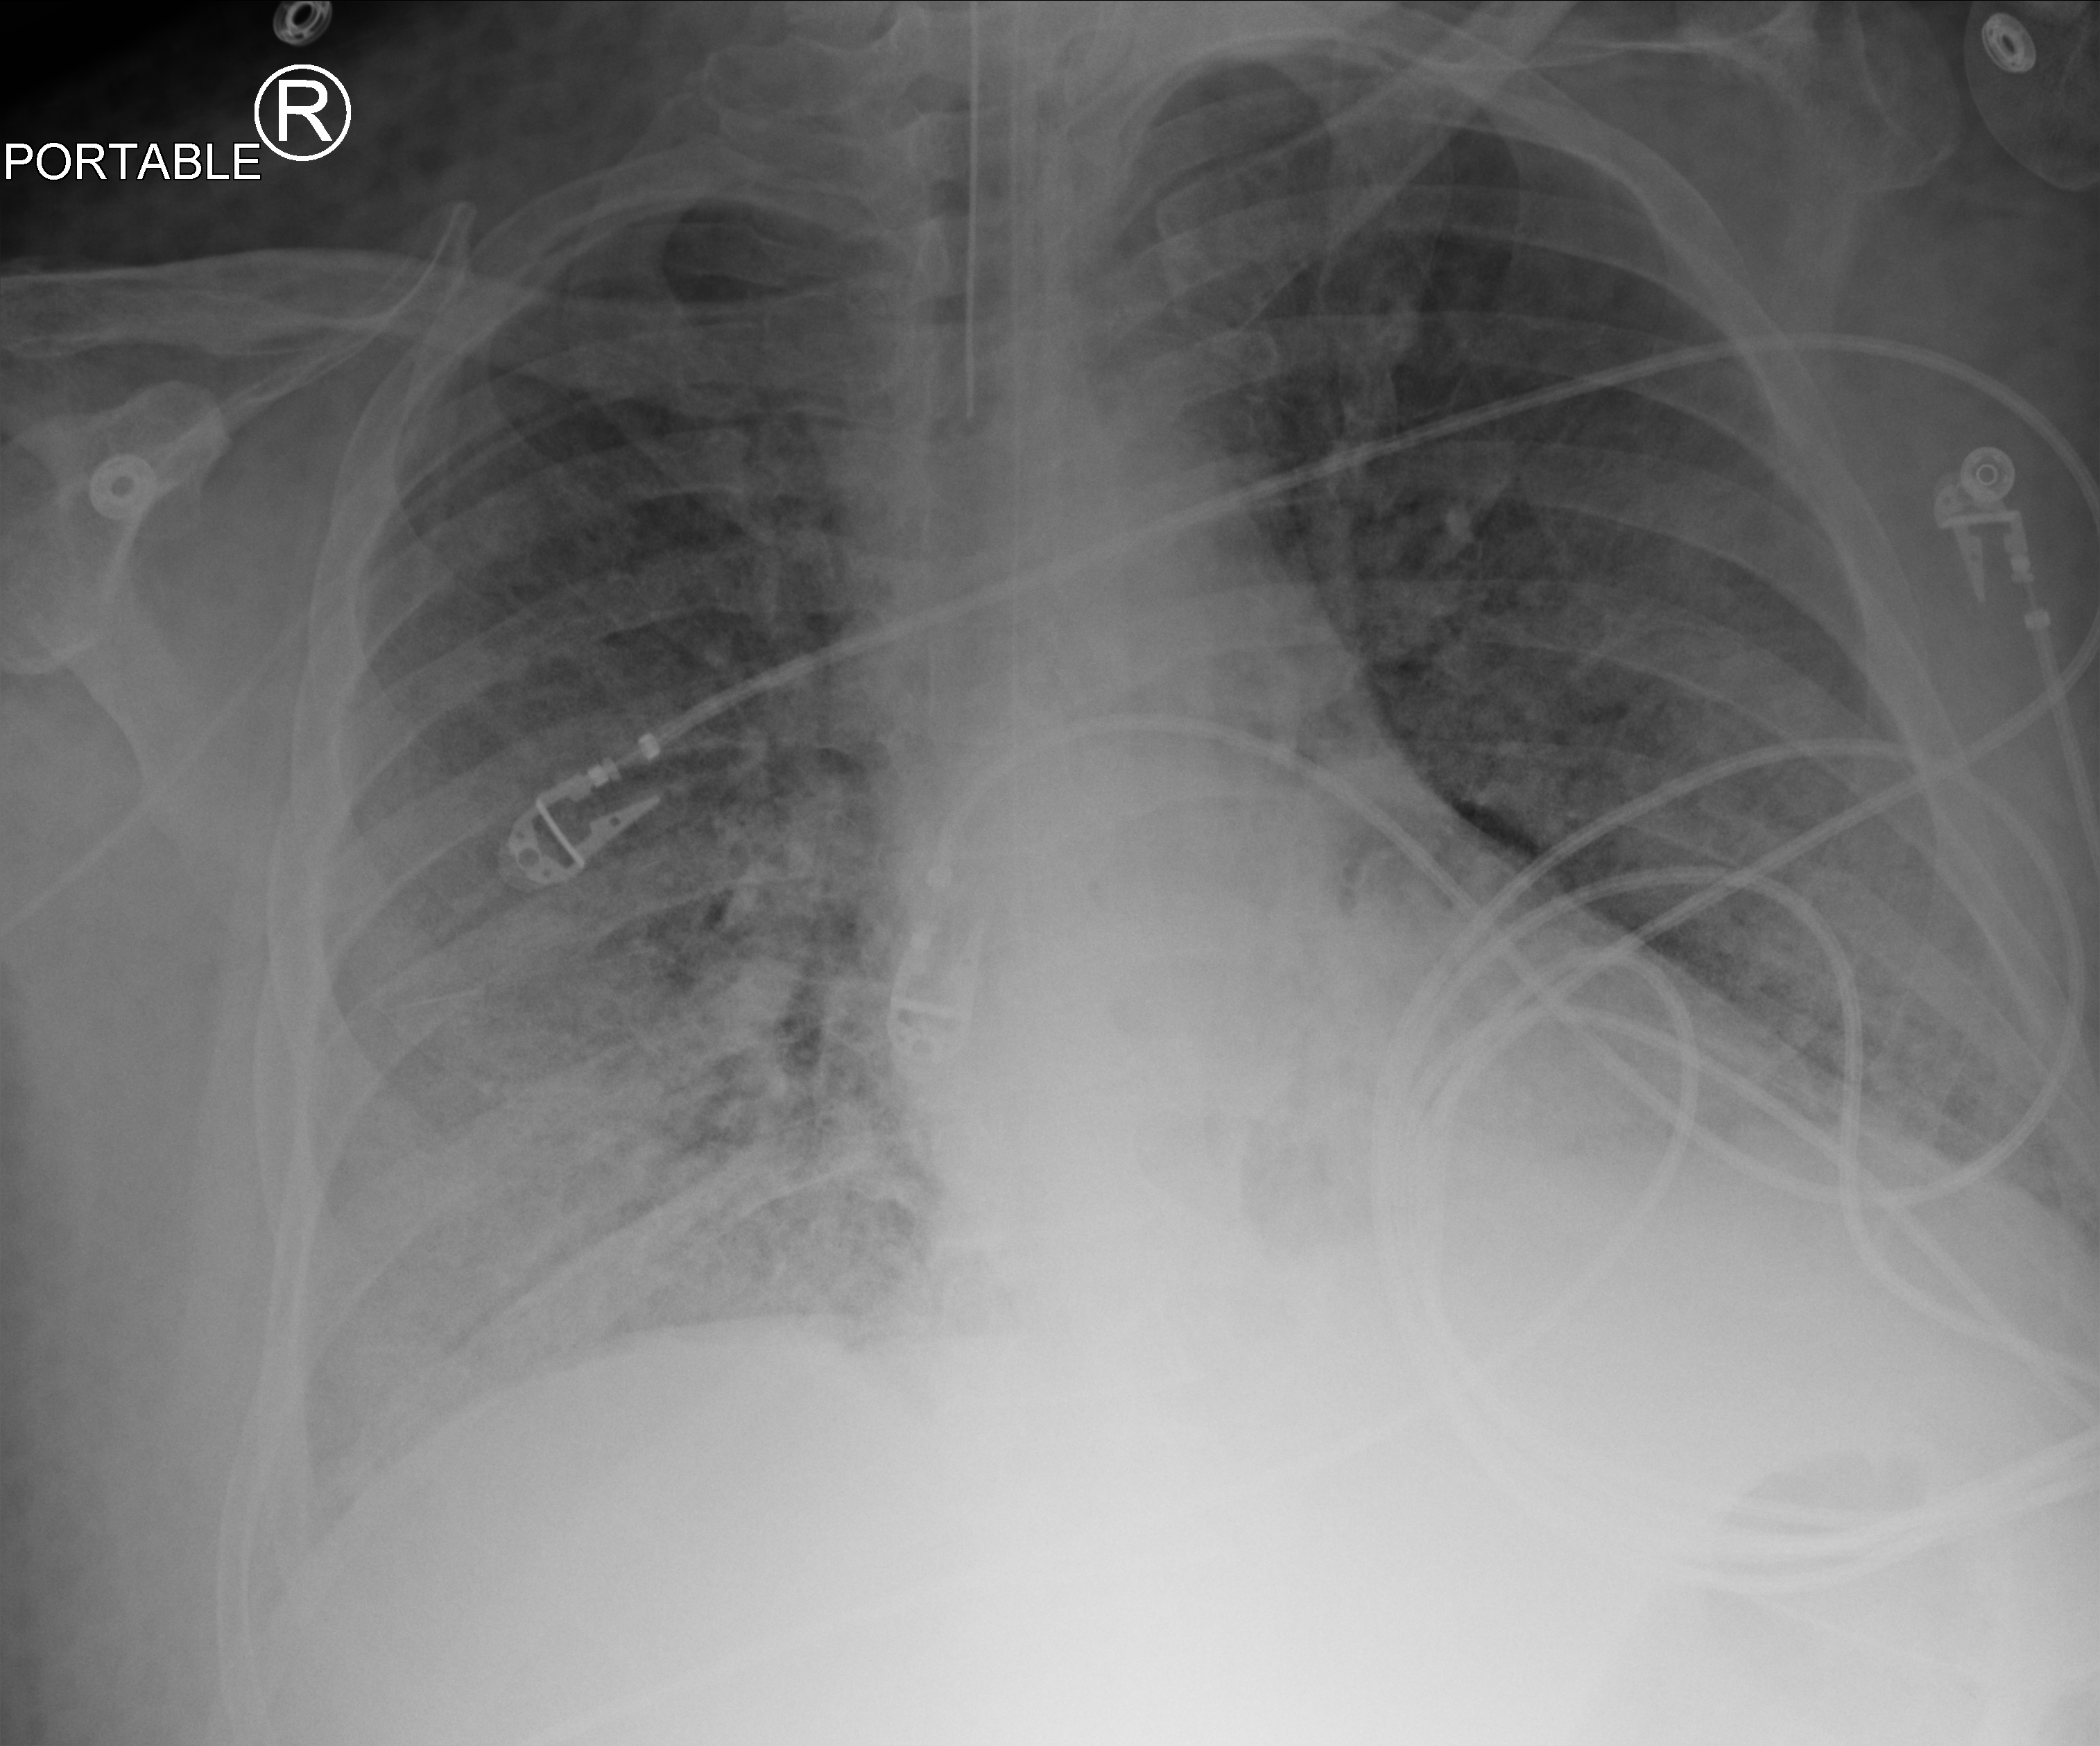
Chest X-ray (portable); anteroposterior (AP) projection. Adult patient hospitalised with COVID-19, age 18–59 years.
Hospital-stay facts (about this admission, not read from this image; timing relative to this image not recorded):
- mechanically ventilated during this hospital stay: yes